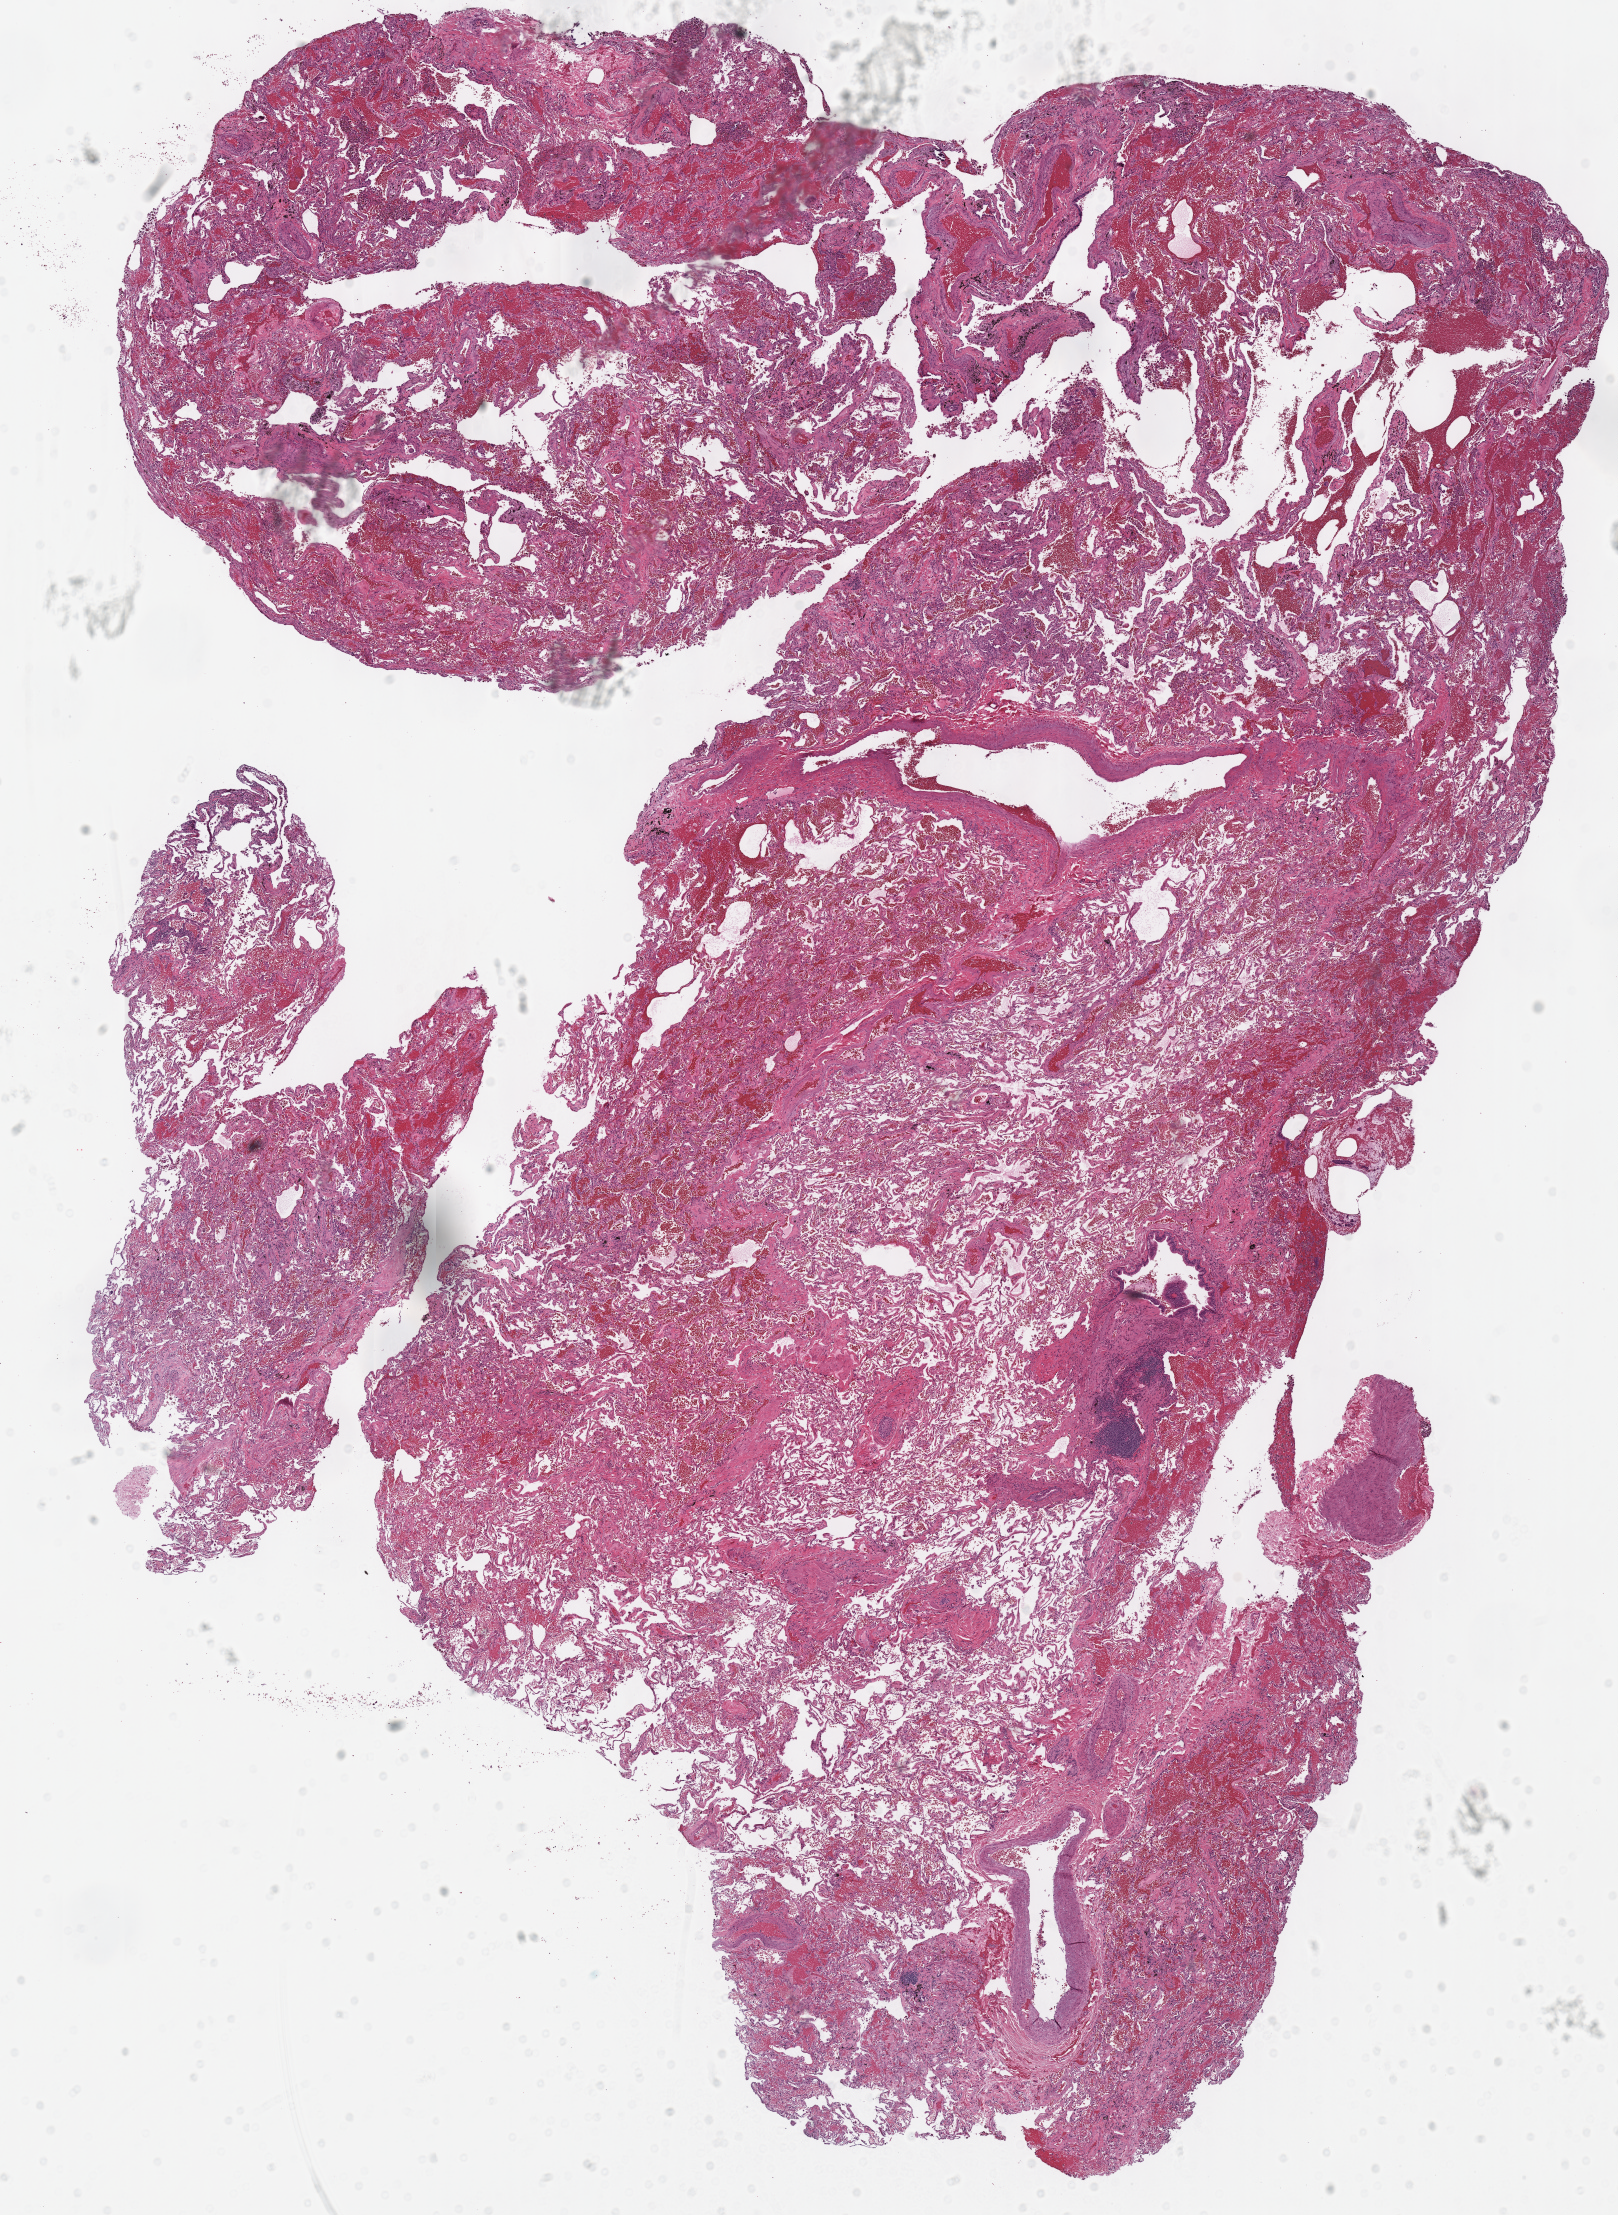
Whole-slide histology image, H&E-stained, whole scanned area (about 12.7 x 17.4 mm, slide scanned at 40x) shown as a low-resolution overview; frozen section from the top of the tissue portion; sample: solid tissue normal (non-tumour tissue), lung. Male, age 70 years at initial diagnosis.
This section: solid tissue normal sample (biorepository sample class). Patient diagnosis: Adenocarcinoma, NOS (upper lobe, lung).